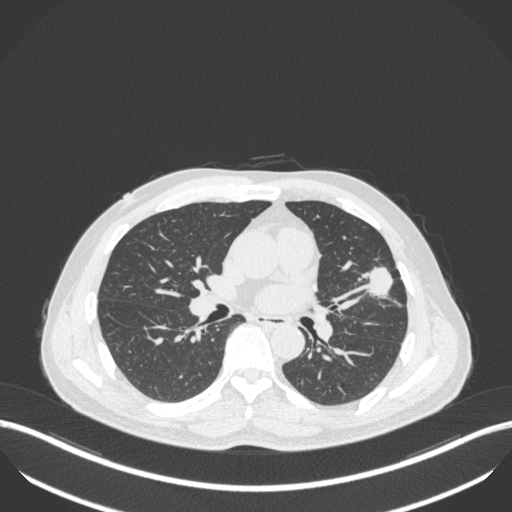
Chest CT, one axial slice; reconstruction kernel B31f; 120 kVp; lung window (W 1500 / L -600 HU); 1 mm slice thickness; 512 × 512 image matrix. Male patient, age 55 years. Case-level facts recorded for this patient, not image findings: clinical TNM (as recorded): T1c N0 M0; histopathological grade: G2-3.
Annotated regions visible in this slice (bounding box drawn by a radiologist):
- lung tumour (recorded histology: adenocarcinoma): bounding box [x1, y1, x2, y2] px = [364, 267, 395, 301]